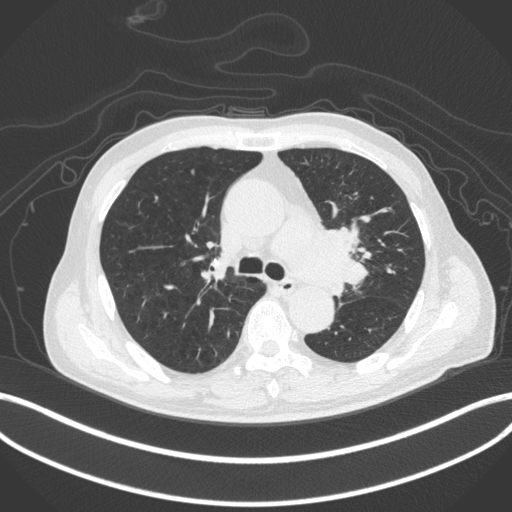
Chest CT, one axial slice; lung window (W 1500 / L -600 HU); 1 mm slice thickness; 512 × 512 image matrix. Patient: male, 77 years. Case-level facts recorded for this patient, not image findings: clinical TNM (as recorded): T3 N1 M0.
Annotated regions visible in this slice (rectangle marked by the reading radiologist):
- lung tumour (recorded histology: adenocarcinoma): bounding box <304,224,369,302> (left, top, right, bottom; pixels)